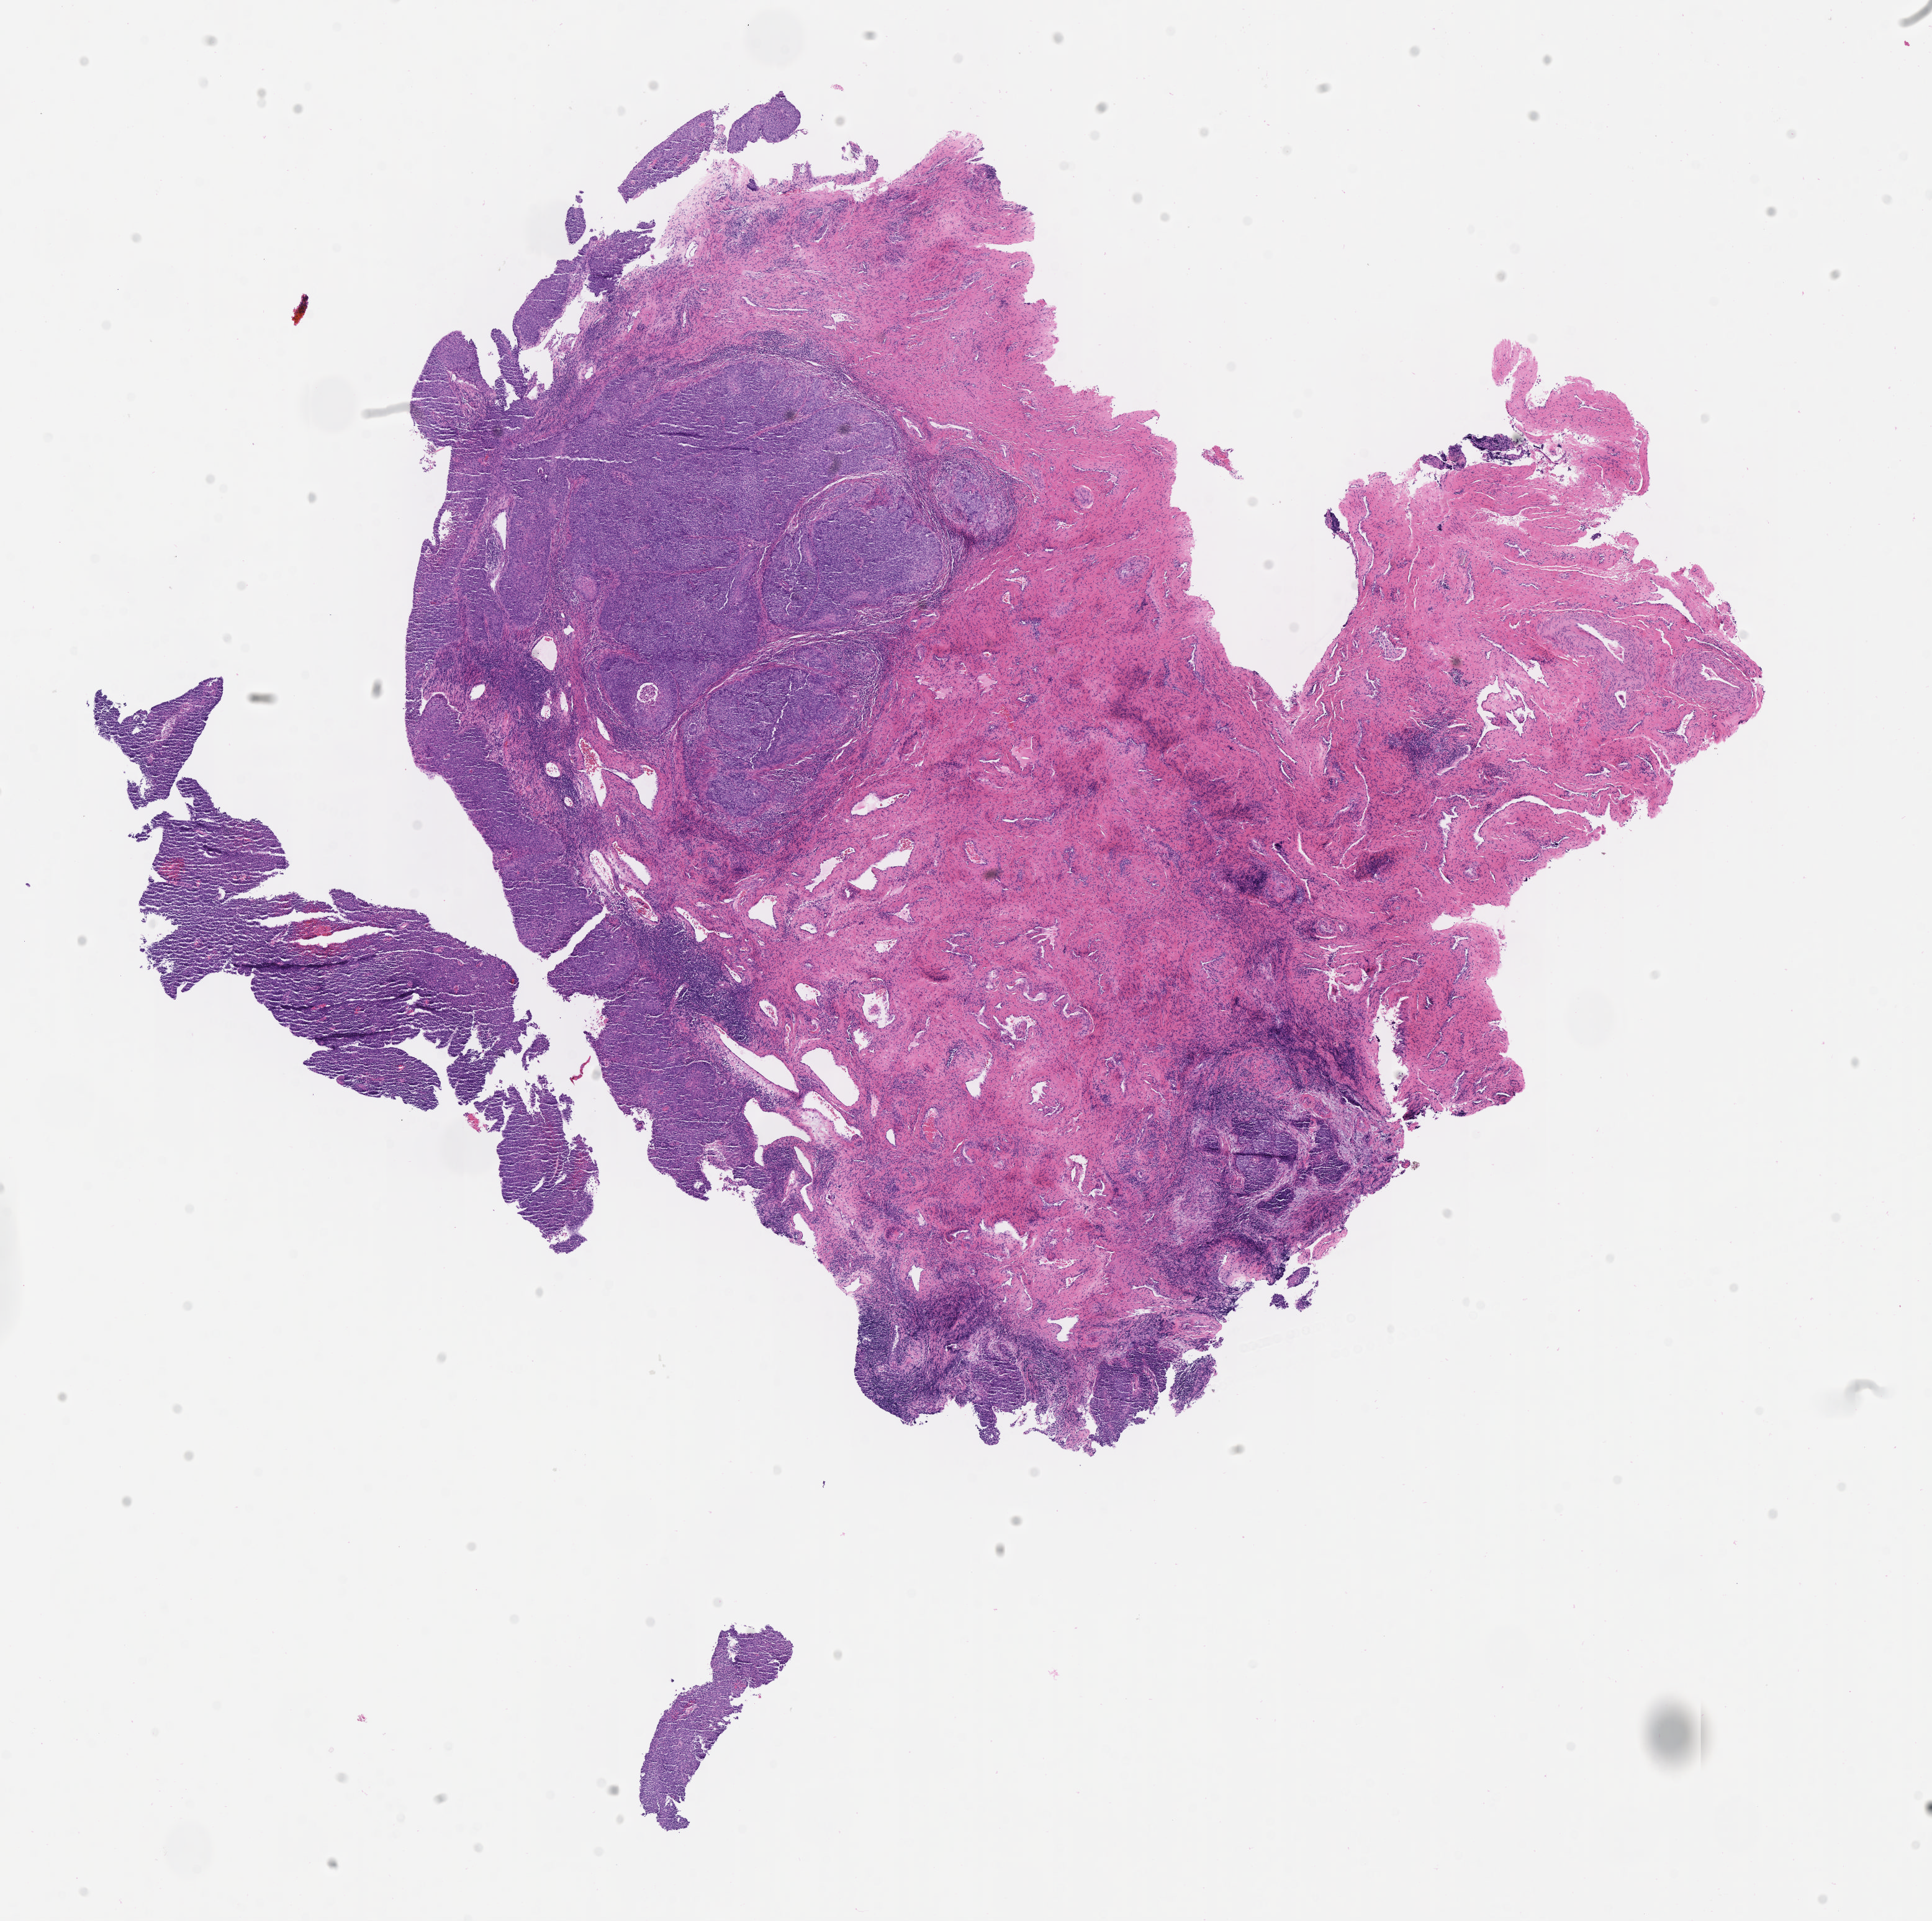
Whole-slide image, haematoxylin and eosin stain — low-resolution overview of the scanned area, about 12.6 x 12.5 mm; specimen: tumor tissue; site: cervix. Patient: female, aged 52.
Diagnosis: Squamous cell carcinoma, large cell, nonkeratinizing, NOS.